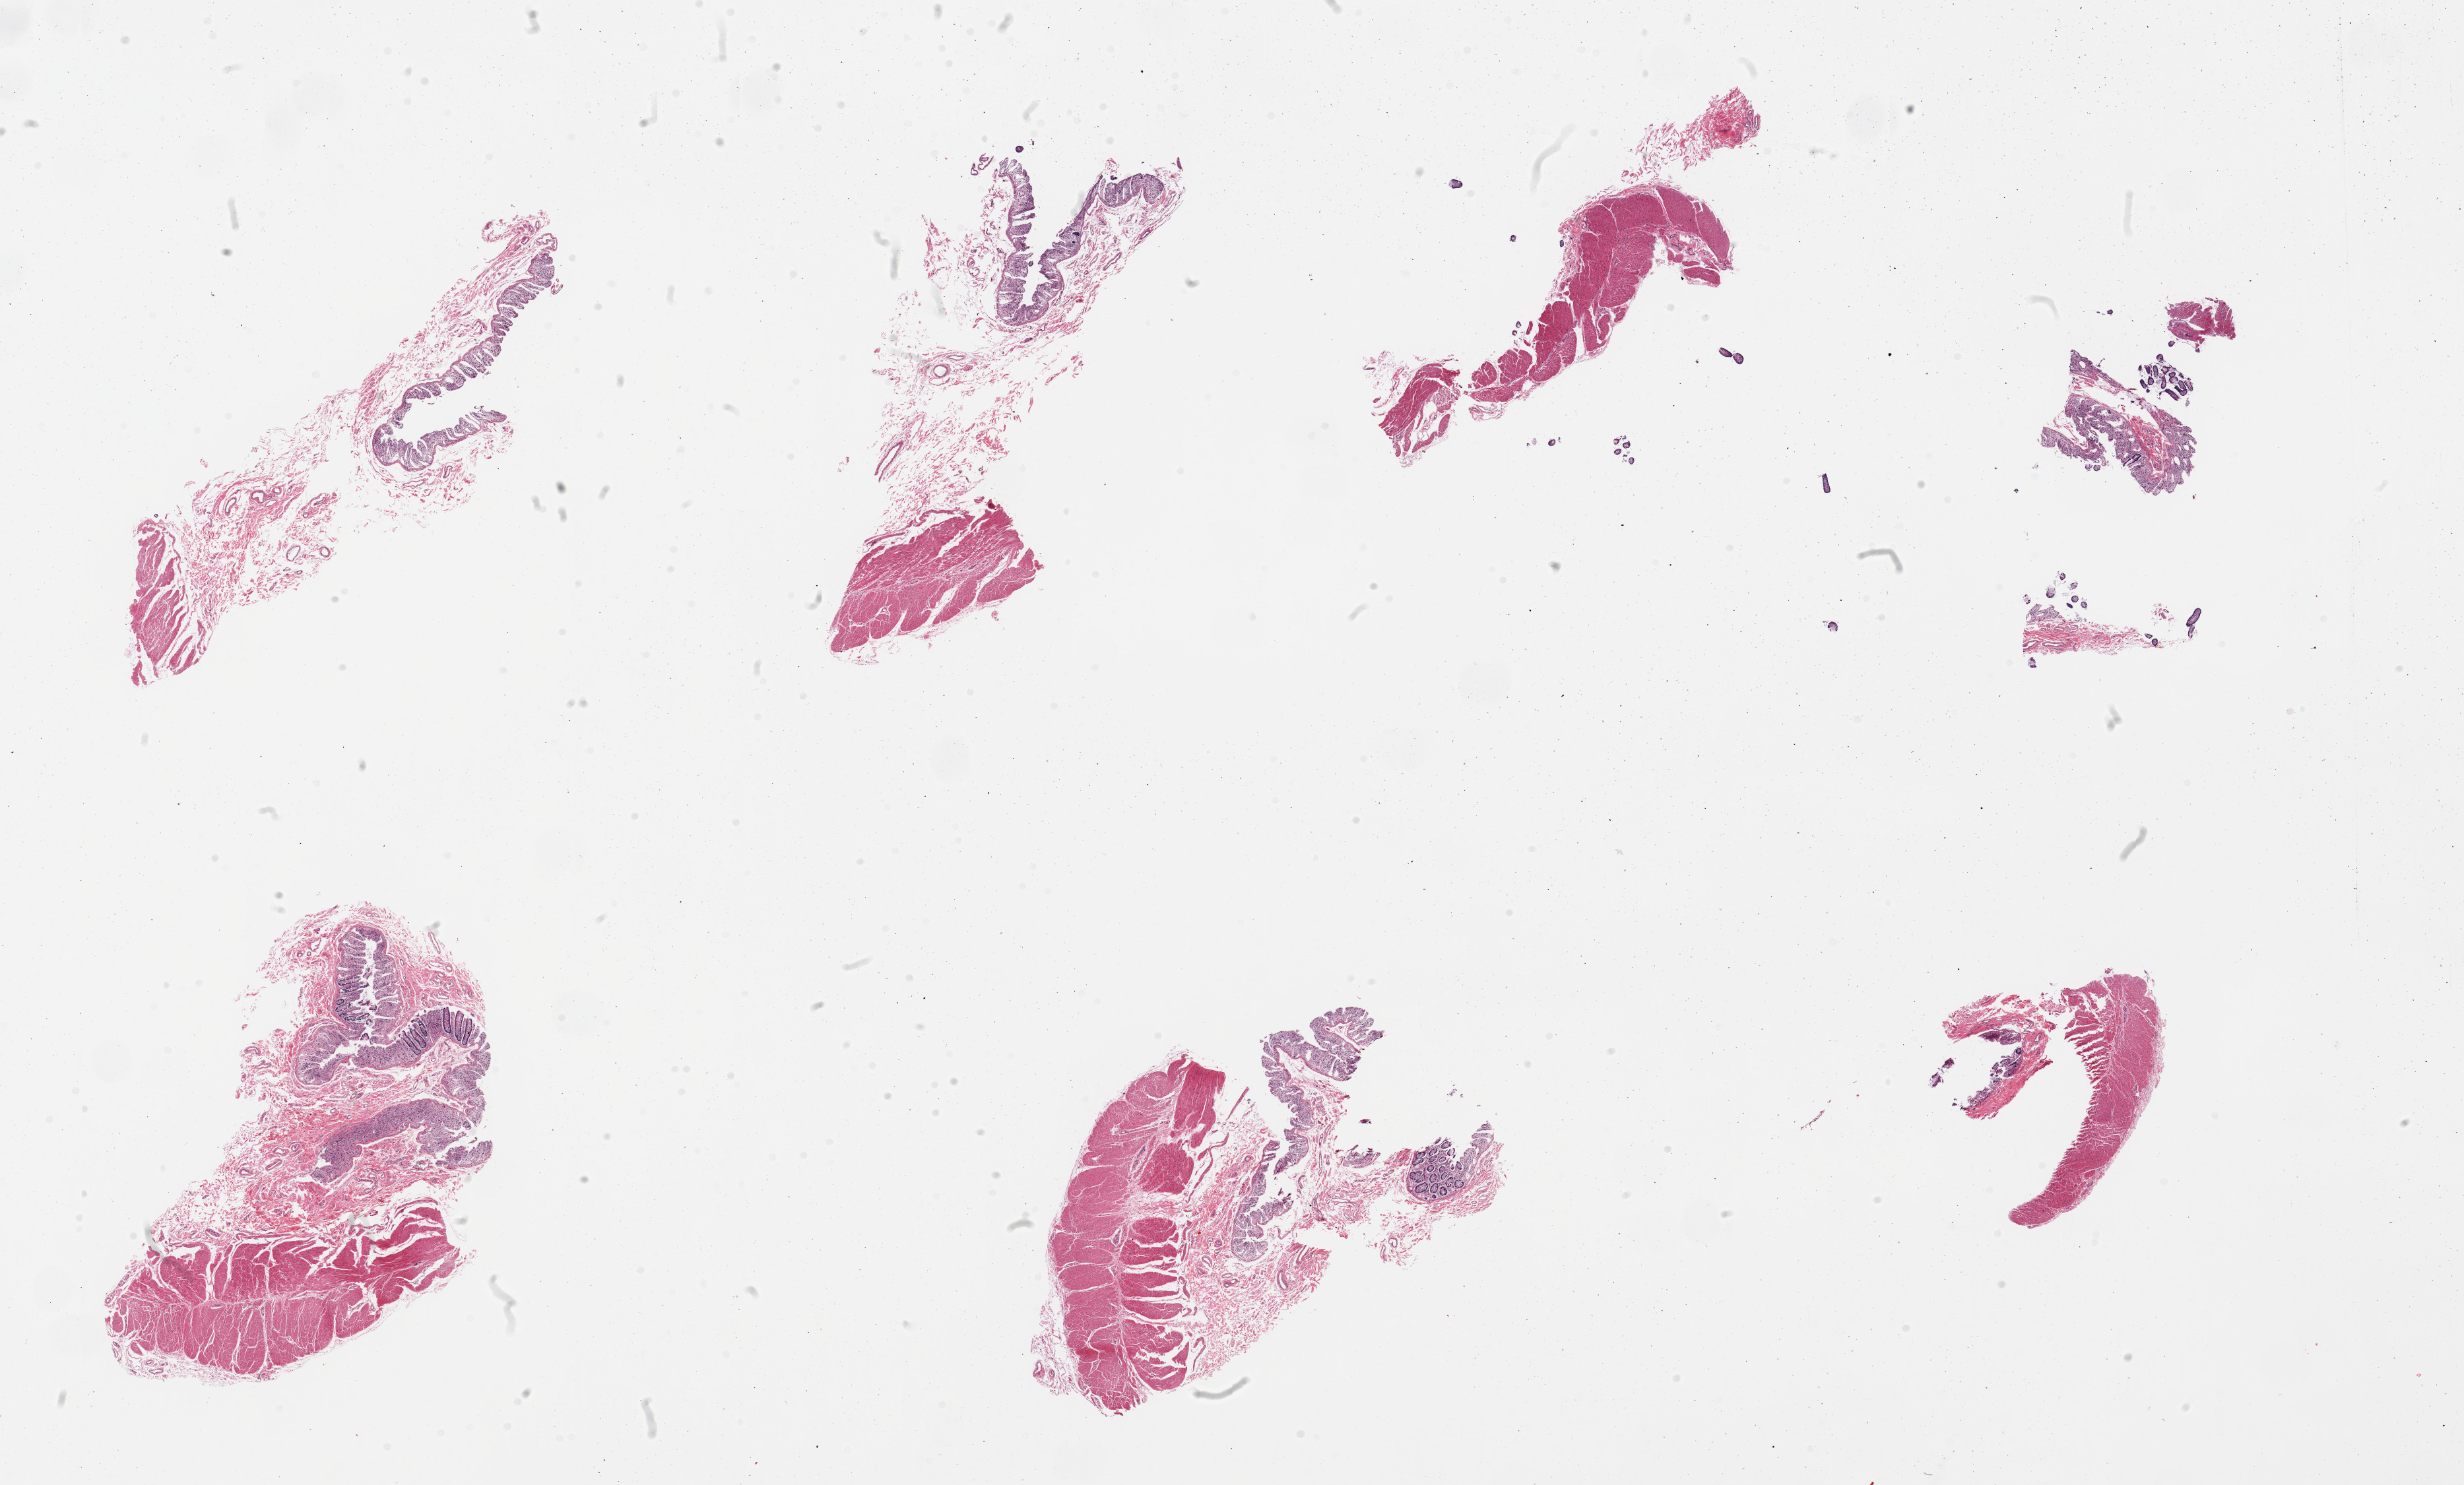
Digitized H&E-stained section — shown as a low-resolution overview of the whole scanned area (about 29.5 x 17.8 mm), PAXgene-fixed, paraffin-embedded tissue, sampled site (target tissue): transverse colon, tissue donor sample. Donor: male.
Pathologist's review note for this sample: 7 fragmented pieces; mucosa autolyzed, muscle preserved.